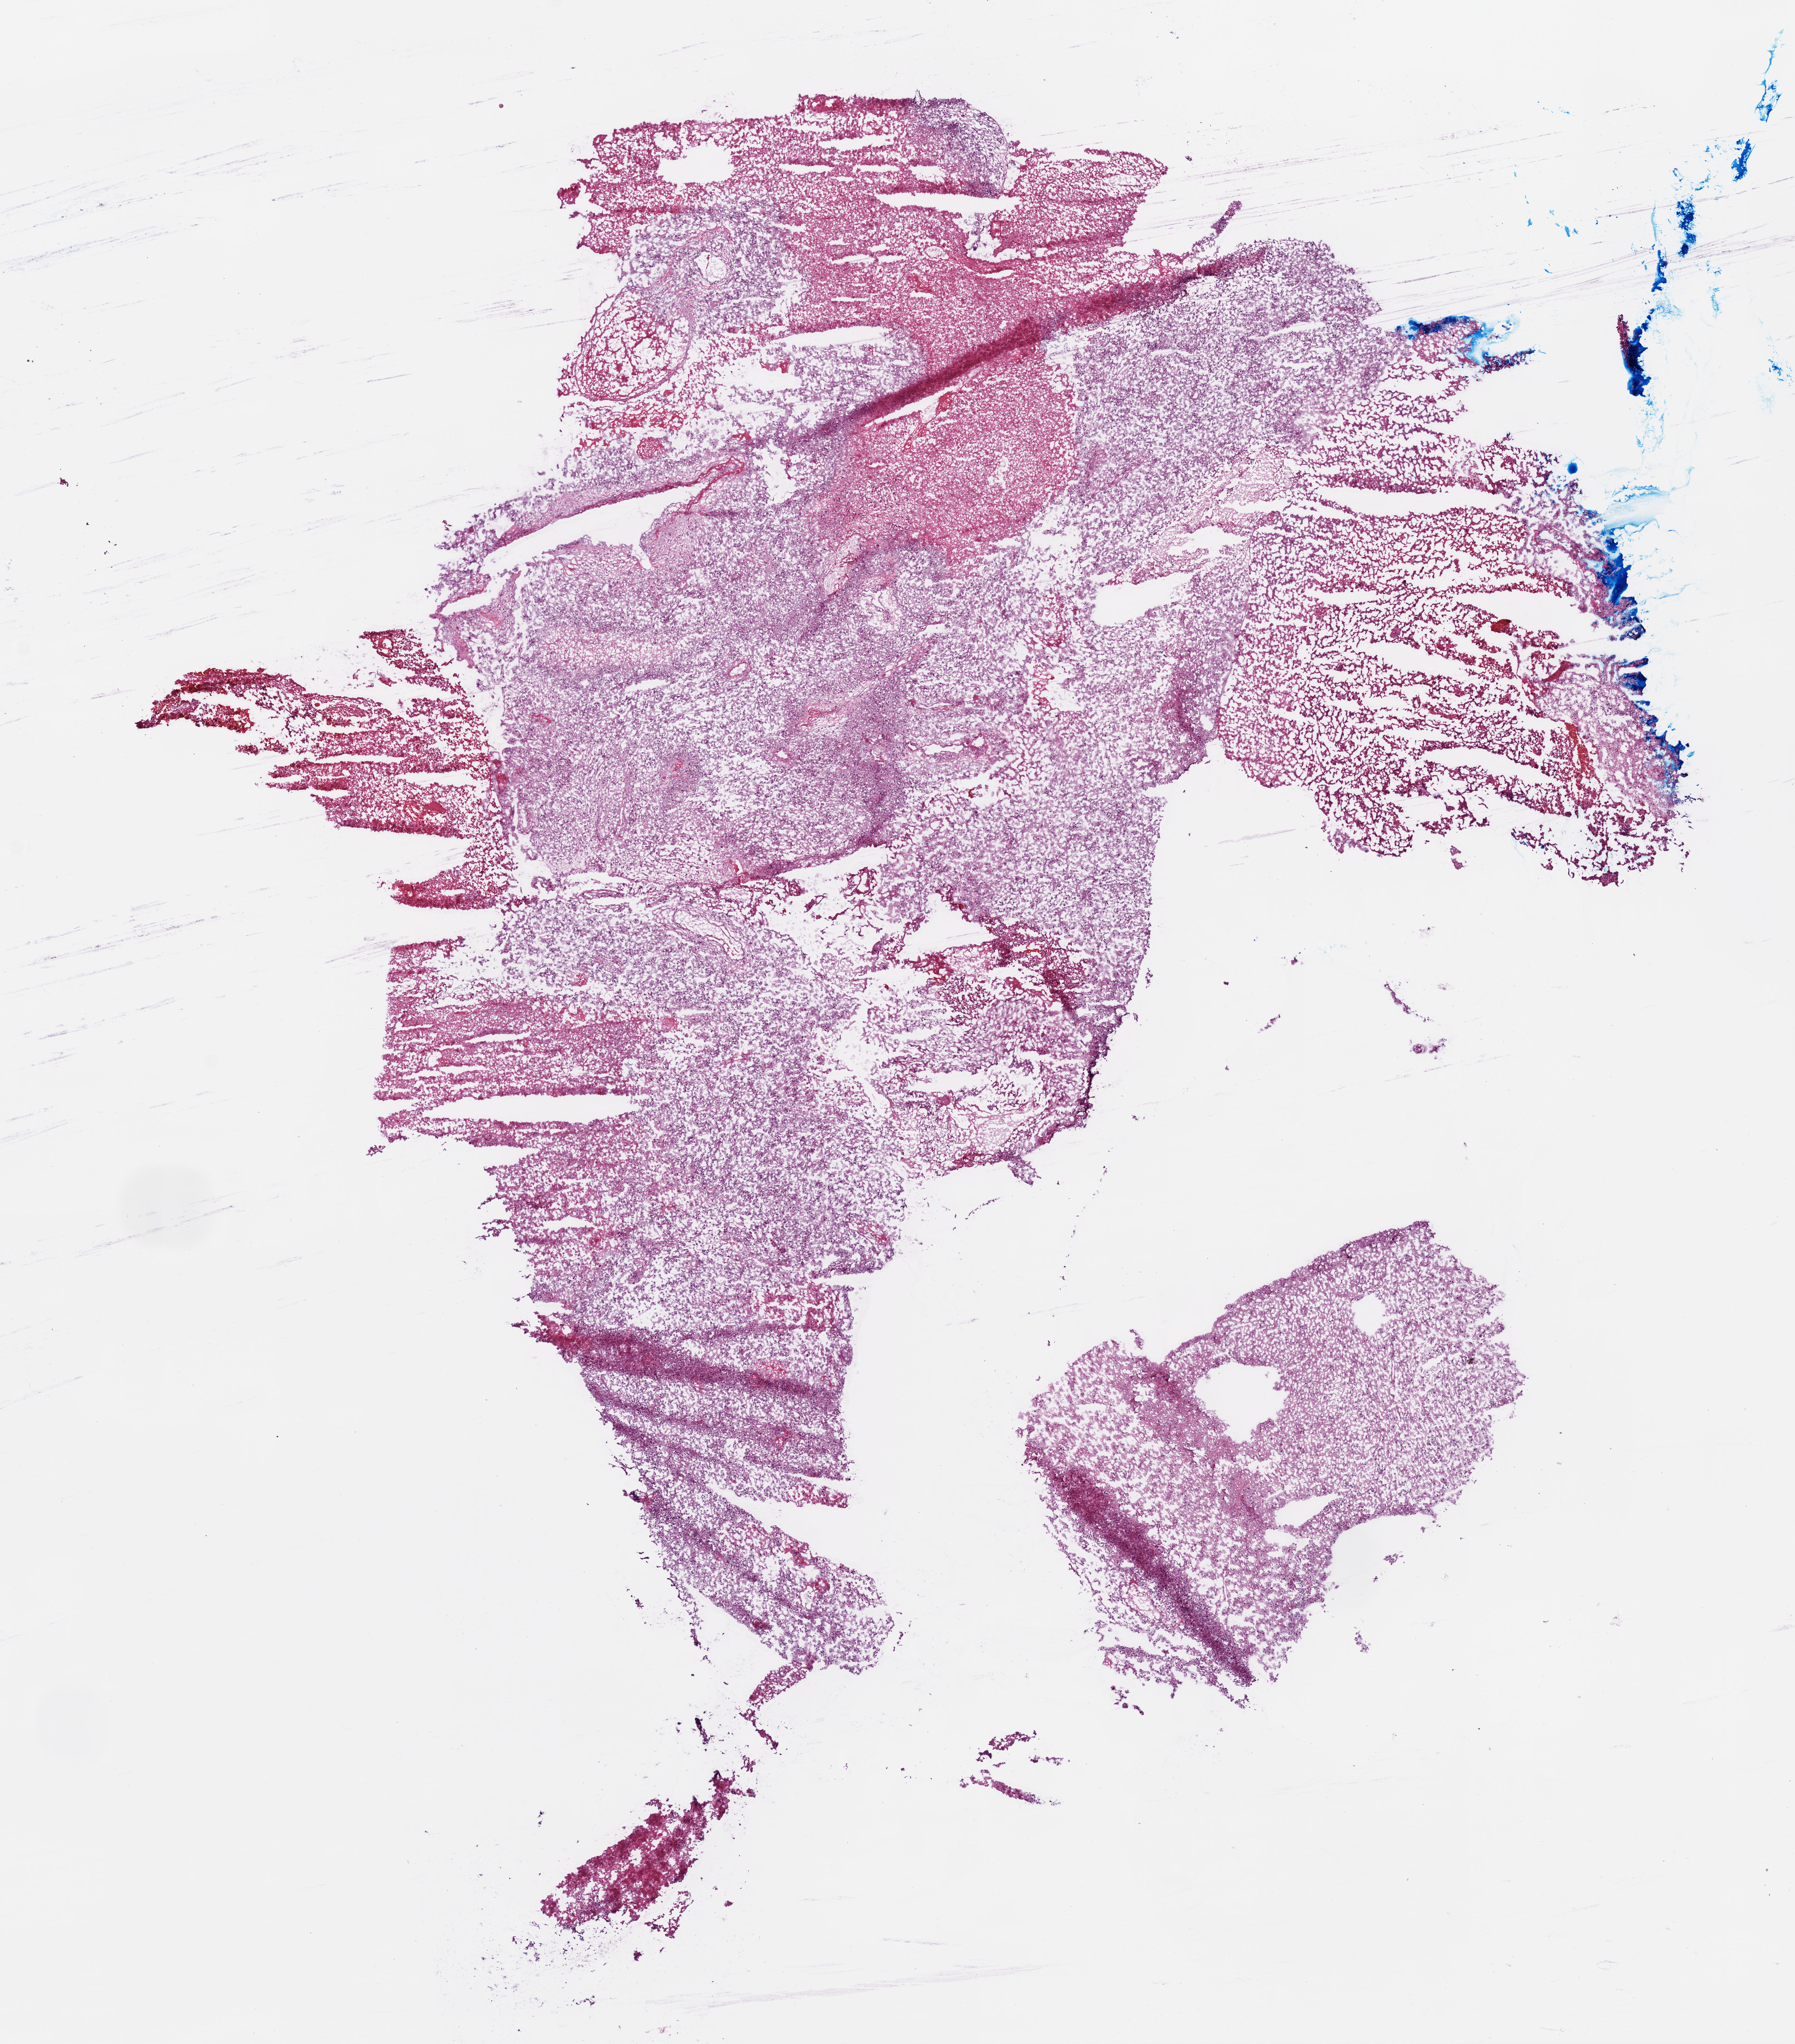
Whole-slide histology image, H&E-stained — low-resolution overview of the scanned area, about 11.0 x 12.6 mm; frozen section from the bottom of the tissue portion; brain, primary tumour sample. Patient: male, age at initial diagnosis 36 years. Composition of this section per pathologist review: tumour cells 70%, tumour nuclei 80%, normal cells 0%, stromal cells 0%, necrosis 30%.
Histologic diagnosis: Glioblastoma.